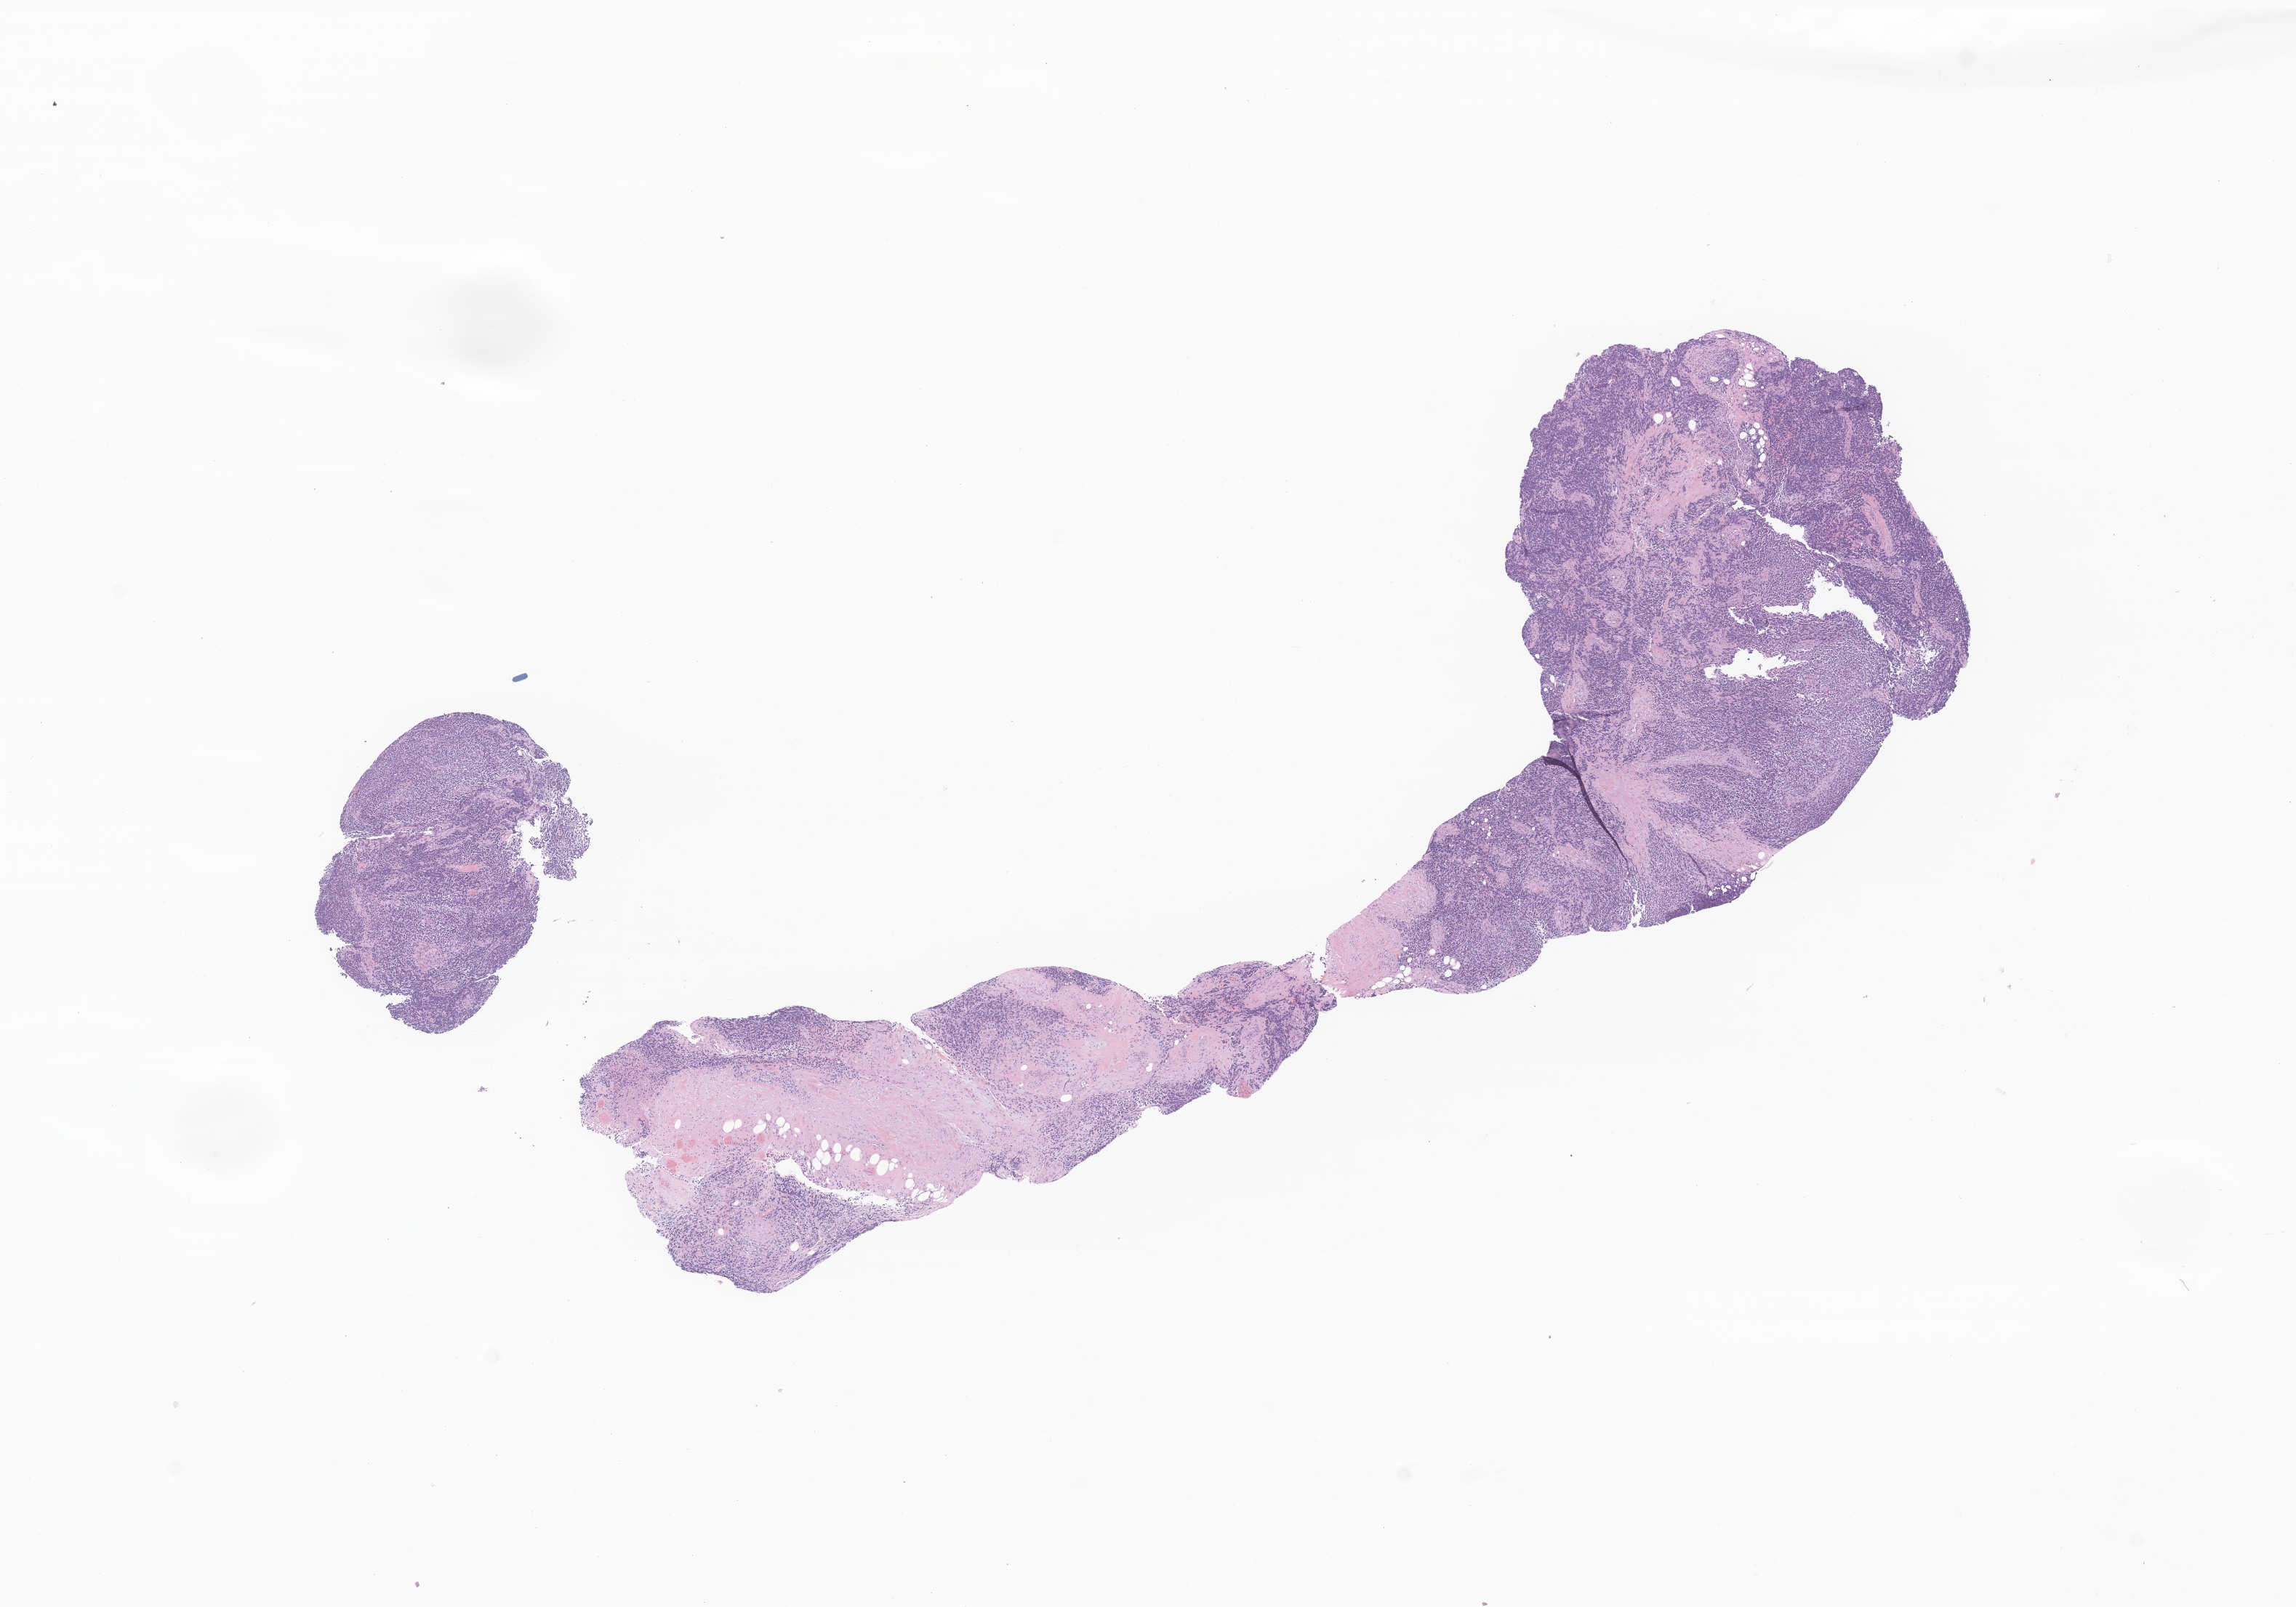
Whole-slide image, hematoxylin and eosin (H&E) stain of tumor tissue from the prostate — a low-resolution overview of the entire scanned area, about 13.3 x 9.3 mm. Formalin-fixed, paraffin-embedded (FFPE) tissue. Male patient, age 79 months.
Diagnosis (ICD-O-3 morphology term): Rhabdomyosarcoma, NOS.